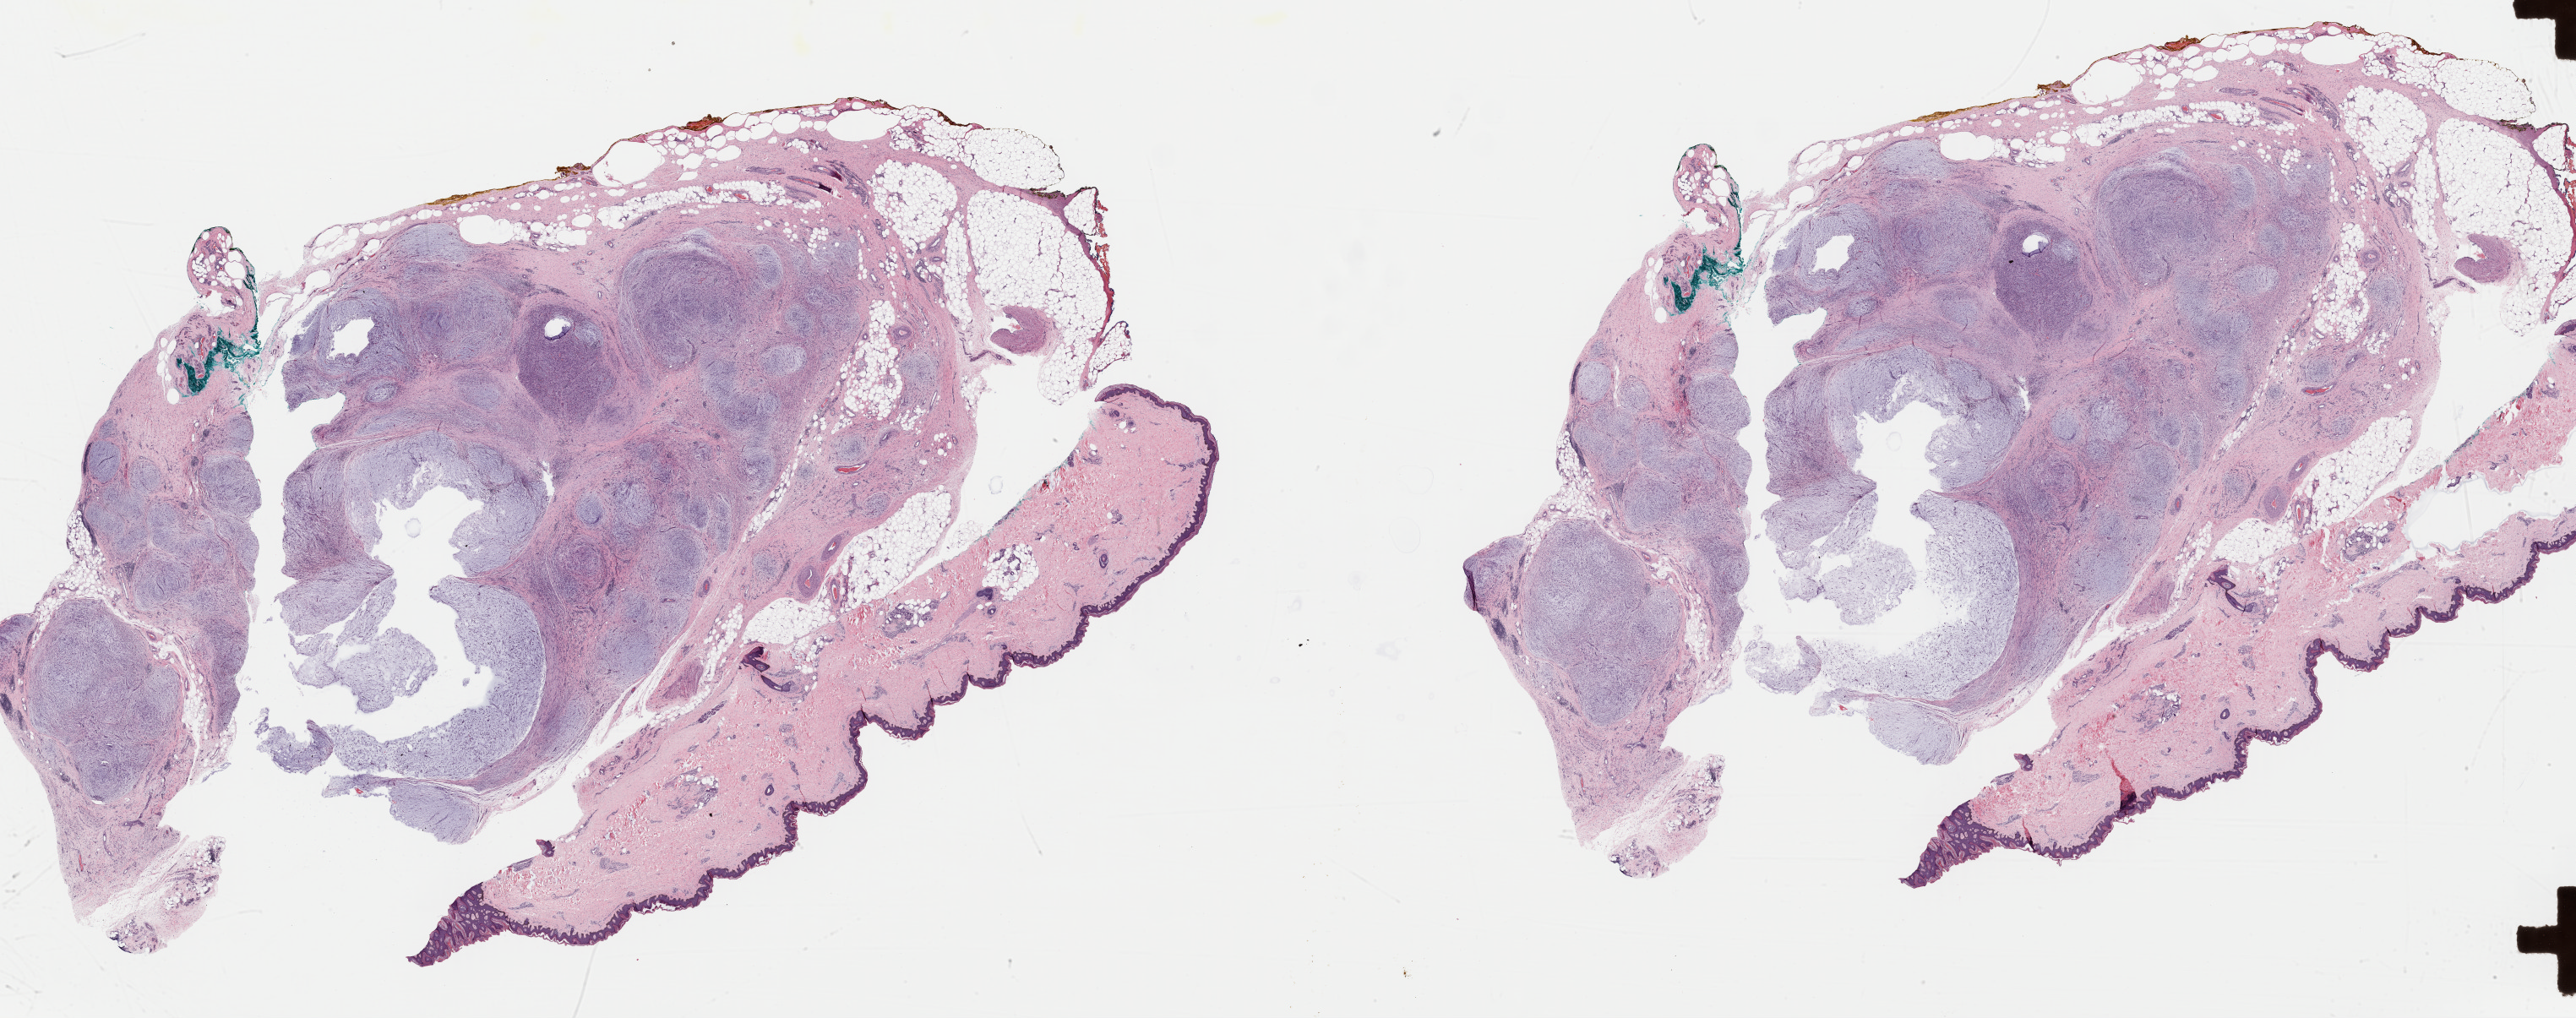
Digitized Hematoxylin and eosin (H&E) stained tissue section (whole slide) — whole scanned area (about 48.2 x 19.0 mm, slide scanned at 40x) shown as a low-resolution overview. Formalin-fixed paraffin-embedded (FFPE) diagnostic section. Sample: primary tumour, connective, subcutaneous and other soft tissues. Female patient; age at initial diagnosis 55 years.
* diagnosis: Fibromyxosarcoma (connective, subcutaneous and other soft tissues of lower limb and hip)